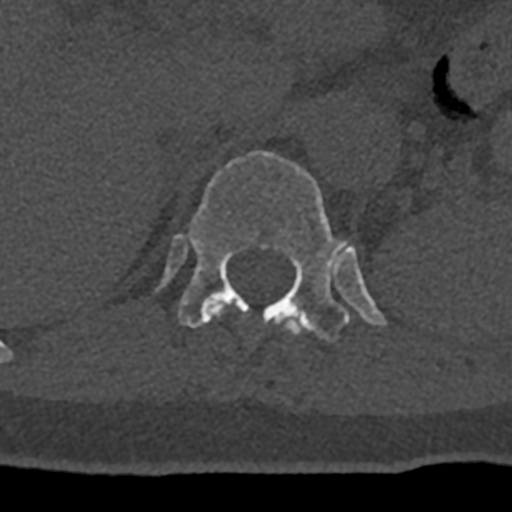
CT including the spine, one axial slice. Slice 504 of 797 in the series (ordered by position). Reconstruction kernel Br40s/3. 120 kVp. Bone window (W 1800 / L 400 HU). 0.5 mm slice thickness. 512 × 512 image matrix, field of view 160 × 160 mm. Patient: male, 74 years. From the clinical record (not read from this slice): primary cancer: renal; vertebrae with lytic lesions (as recorded): T10, L1, L2, L3, L4, L5.
Annotated regions visible in this slice (semi-automatically segmented with operator editing):
- T11 vertebra: bounding box <210,304,304,335> (left, top, right, bottom; pixels)
- T12 vertebra: <156,151,387,342>